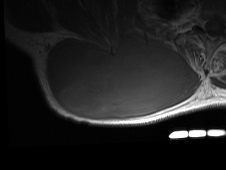
MRI of an extremity soft-tissue mass, one axial slice; MR volume resampled by the dataset authors to the PET/CT grid (not the native acquisition matrix); 226 × 170 image matrix, field of view 221 × 166 mm. Male patient. Case-level facts recorded for this patient, not image findings: histological type: pleiomorphic spindle cell undifferentiated; grade: high; site of the primary tumour: right parascapusular.
Outlined on this slice (expert contour drawn on MRI and transferred to this co-registered scan by the dataset authors):
- gross tumour volume including surrounding oedema: box from (x=44, y=33) to (x=198, y=121) px
- gross tumour volume (mass): (x=46, y=38)–(x=186, y=119)